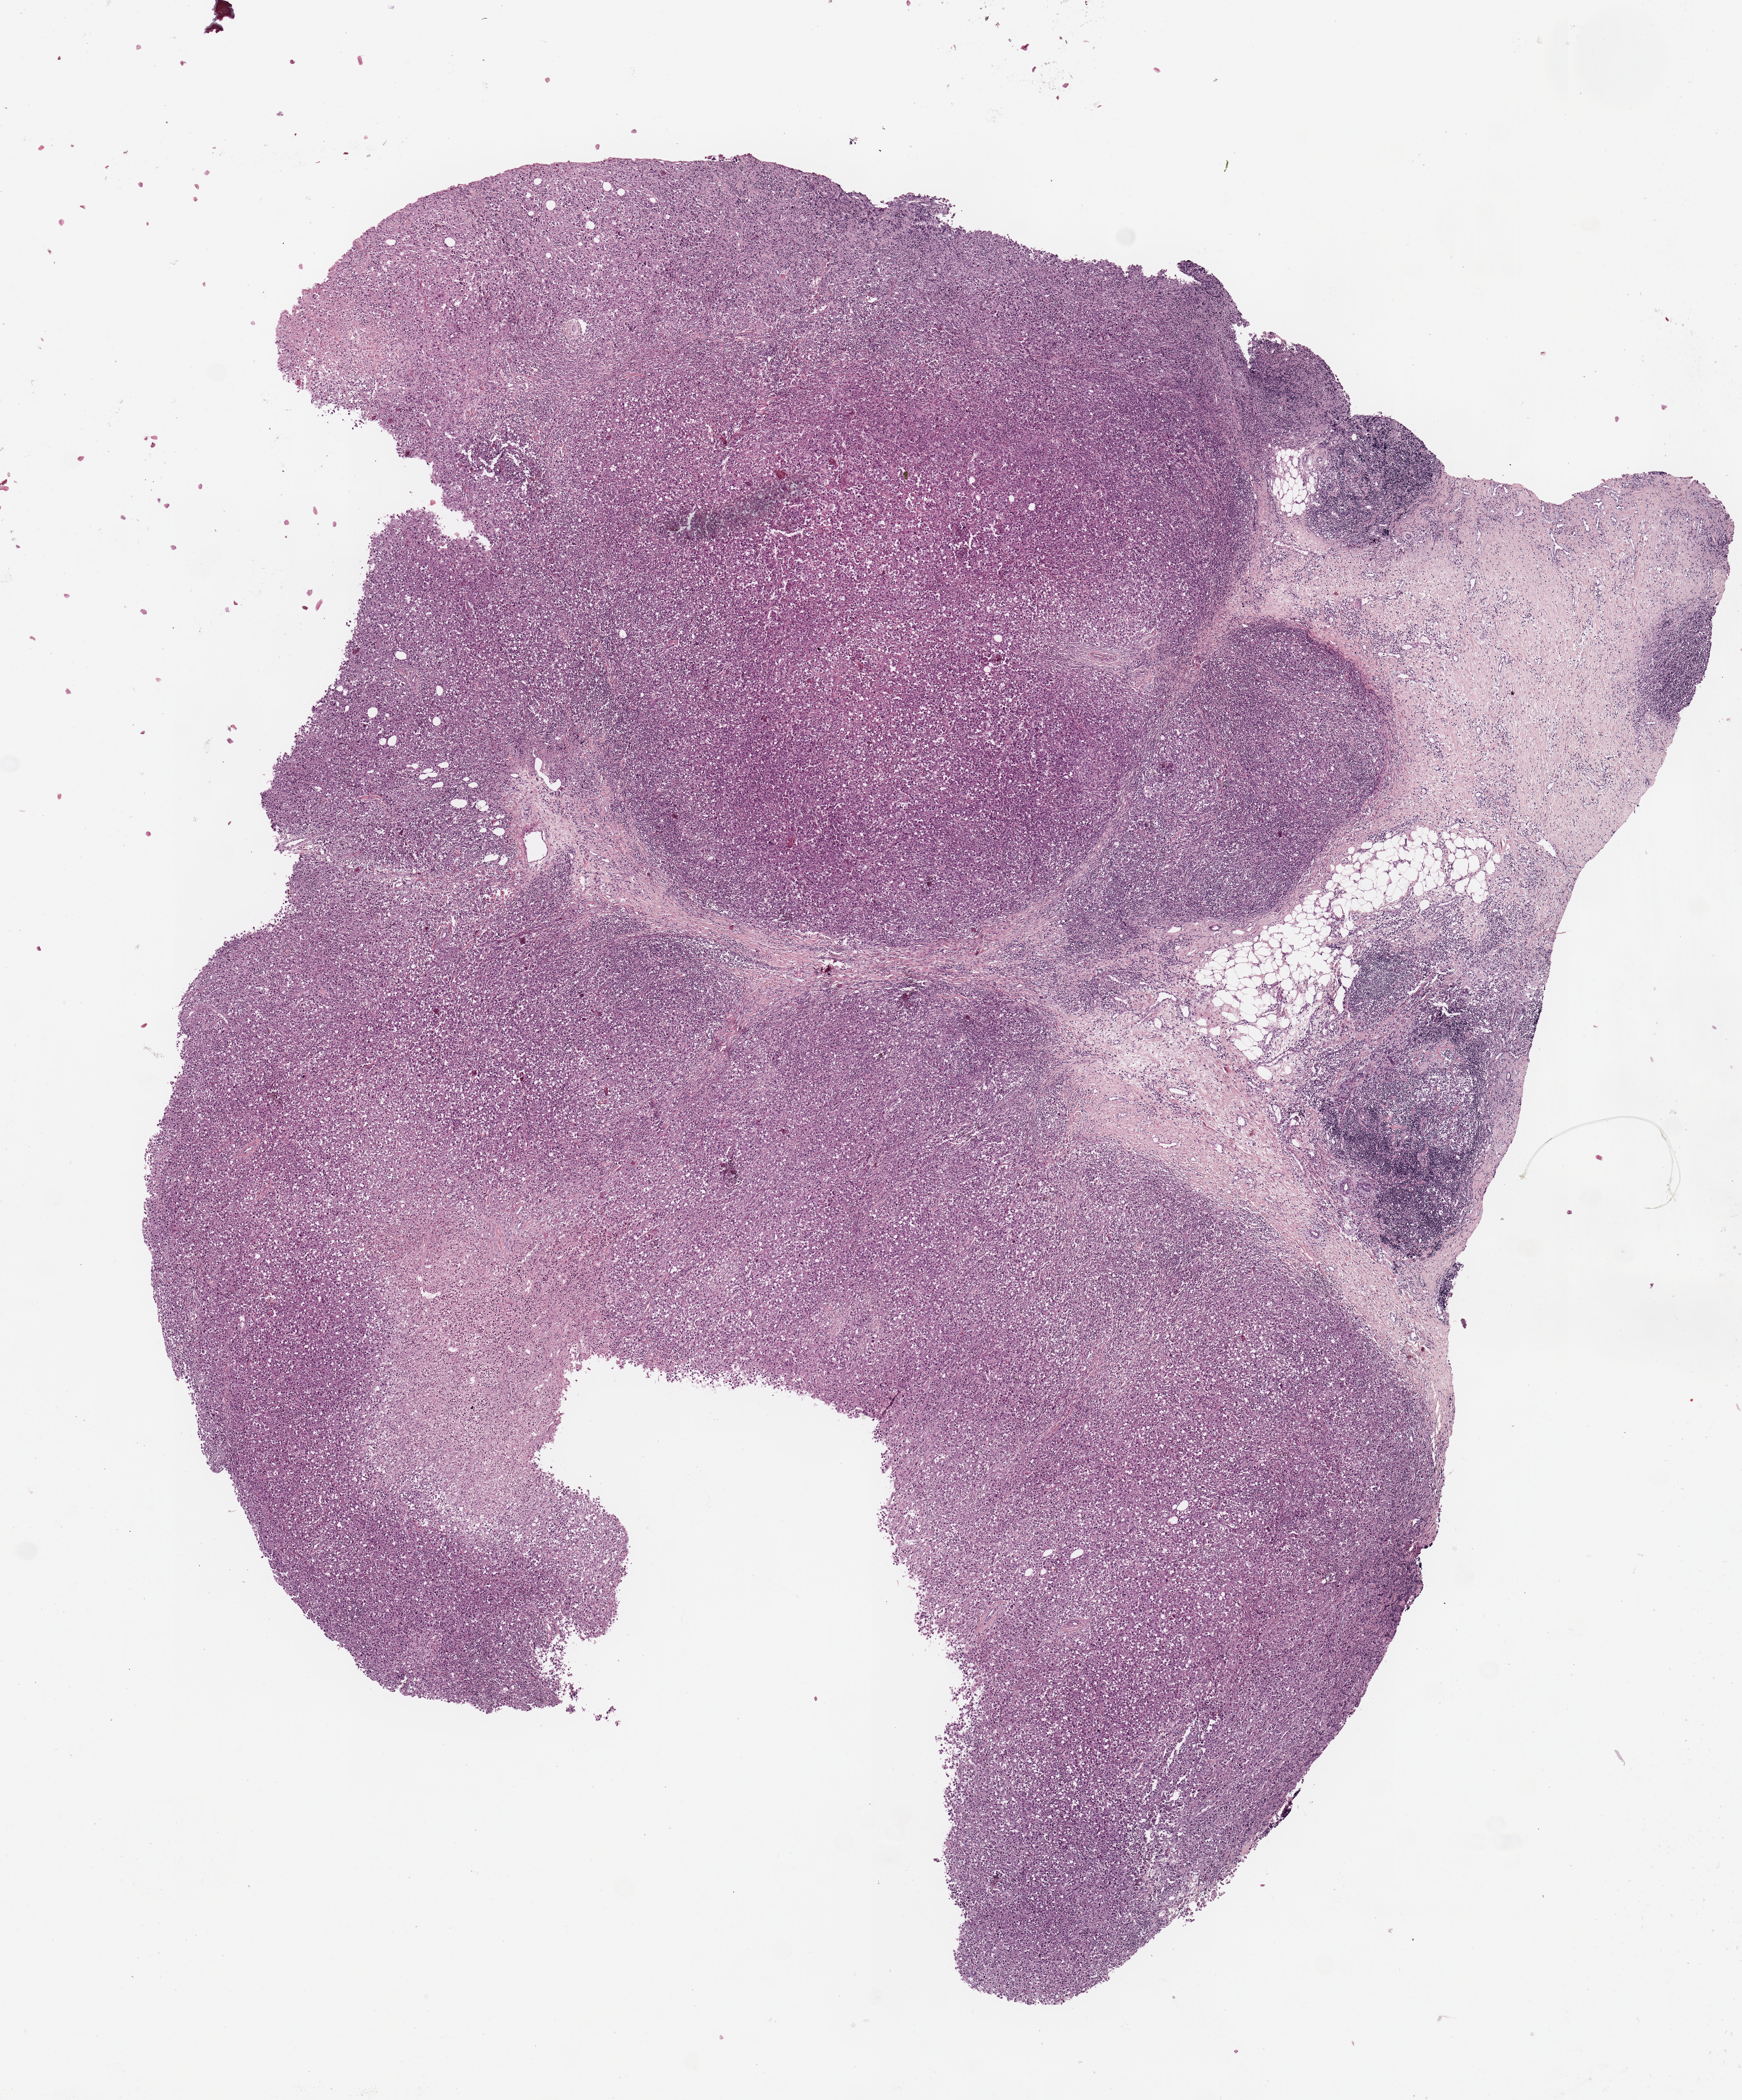
Whole-slide histology image, H&E-stained — shown as a low-resolution overview of the whole scanned area (about 9.8 x 11.9 mm, slide scanned at 20x), tumour tissue sample, sampled site: lymph node. 76-year-old male patient. Slide review estimates, as recorded: tumour nuclei 90%, necrosis 0%.
This section: metastatic tumour tissue. Patient diagnosis: Malignant melanoma, NOS. Primary tumour site (as recorded): extremities.